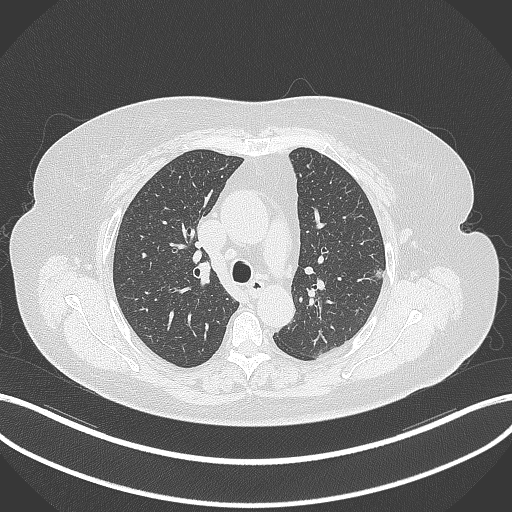
Chest CT, one axial slice; slice 221 of 309 in the series (ordered by position); reconstruction kernel B70f; 120 kVp; lung window (W 1500 / L -600 HU); 1 mm slice thickness; 512 × 512 image matrix, field of view 400 × 400 mm. Patient: female, 70 years. From the clinical record (not read from this slice): clinical TNM (as recorded): T1c N0 M0.
Outlined on this slice (rectangle marked by the reading radiologist):
- lung tumour (recorded histology: adenocarcinoma): bounding box (x1, y1, x2, y2) in pixels: (373, 266, 387, 281)